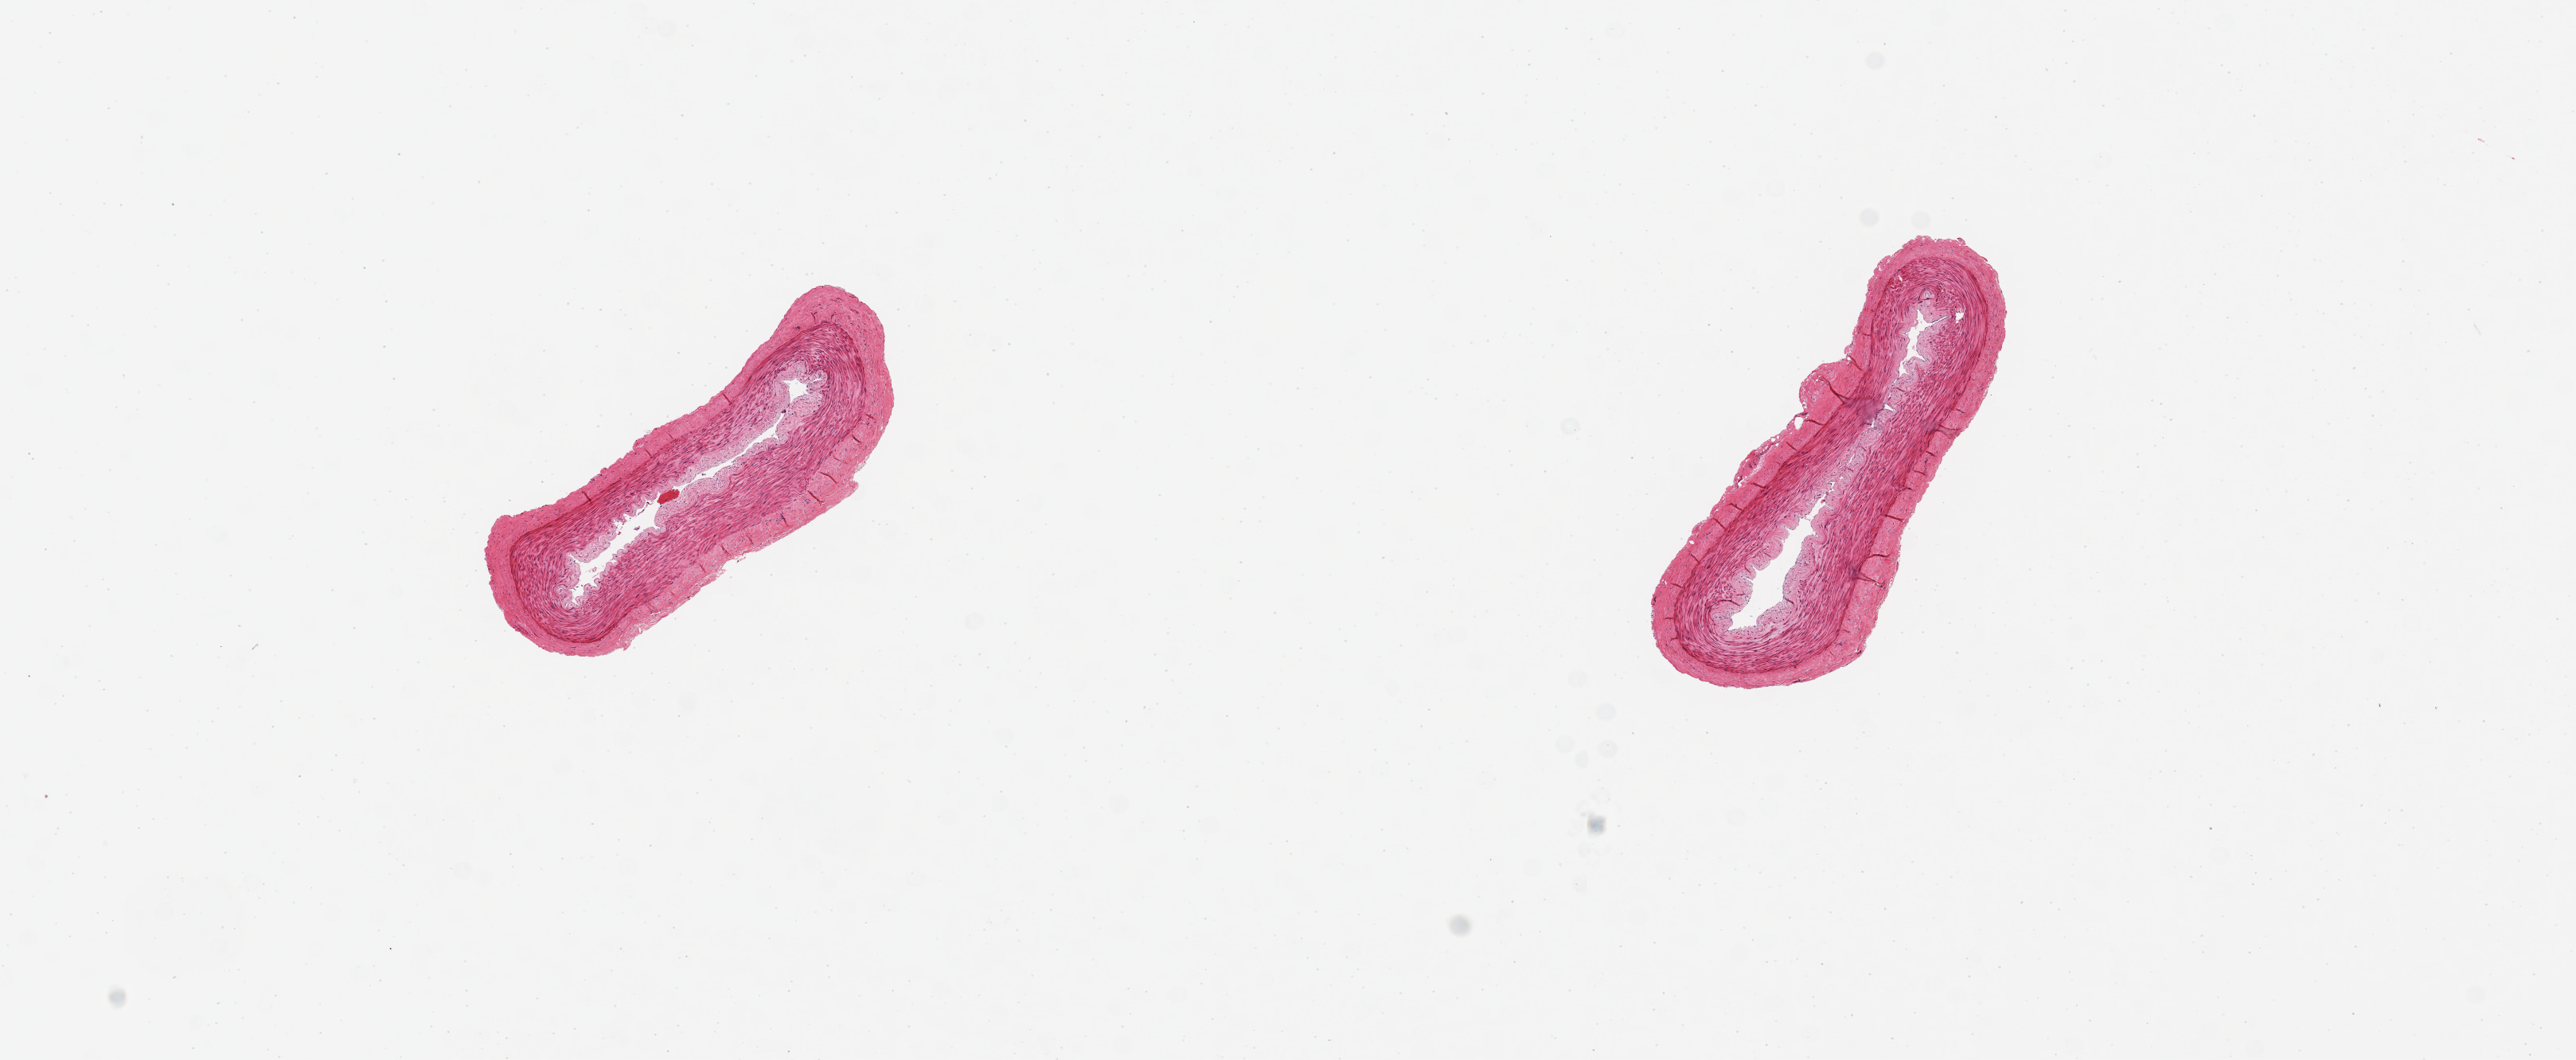
Whole-slide image, hematoxylin and eosin (H&E) stain, brightfield, whole scanned area (about 12.8 x 5.3 mm, slide scanned at 20x) shown as a low-resolution overview, PAXgene-fixed, paraffin-embedded tissue, section of tibial artery (target tissue), tissue donor sample. Donor: male.
Reviewer comment on this tissue sample: 2 aliquots, ~1.5mm in d. Good, clean specimens, no adherent fat.